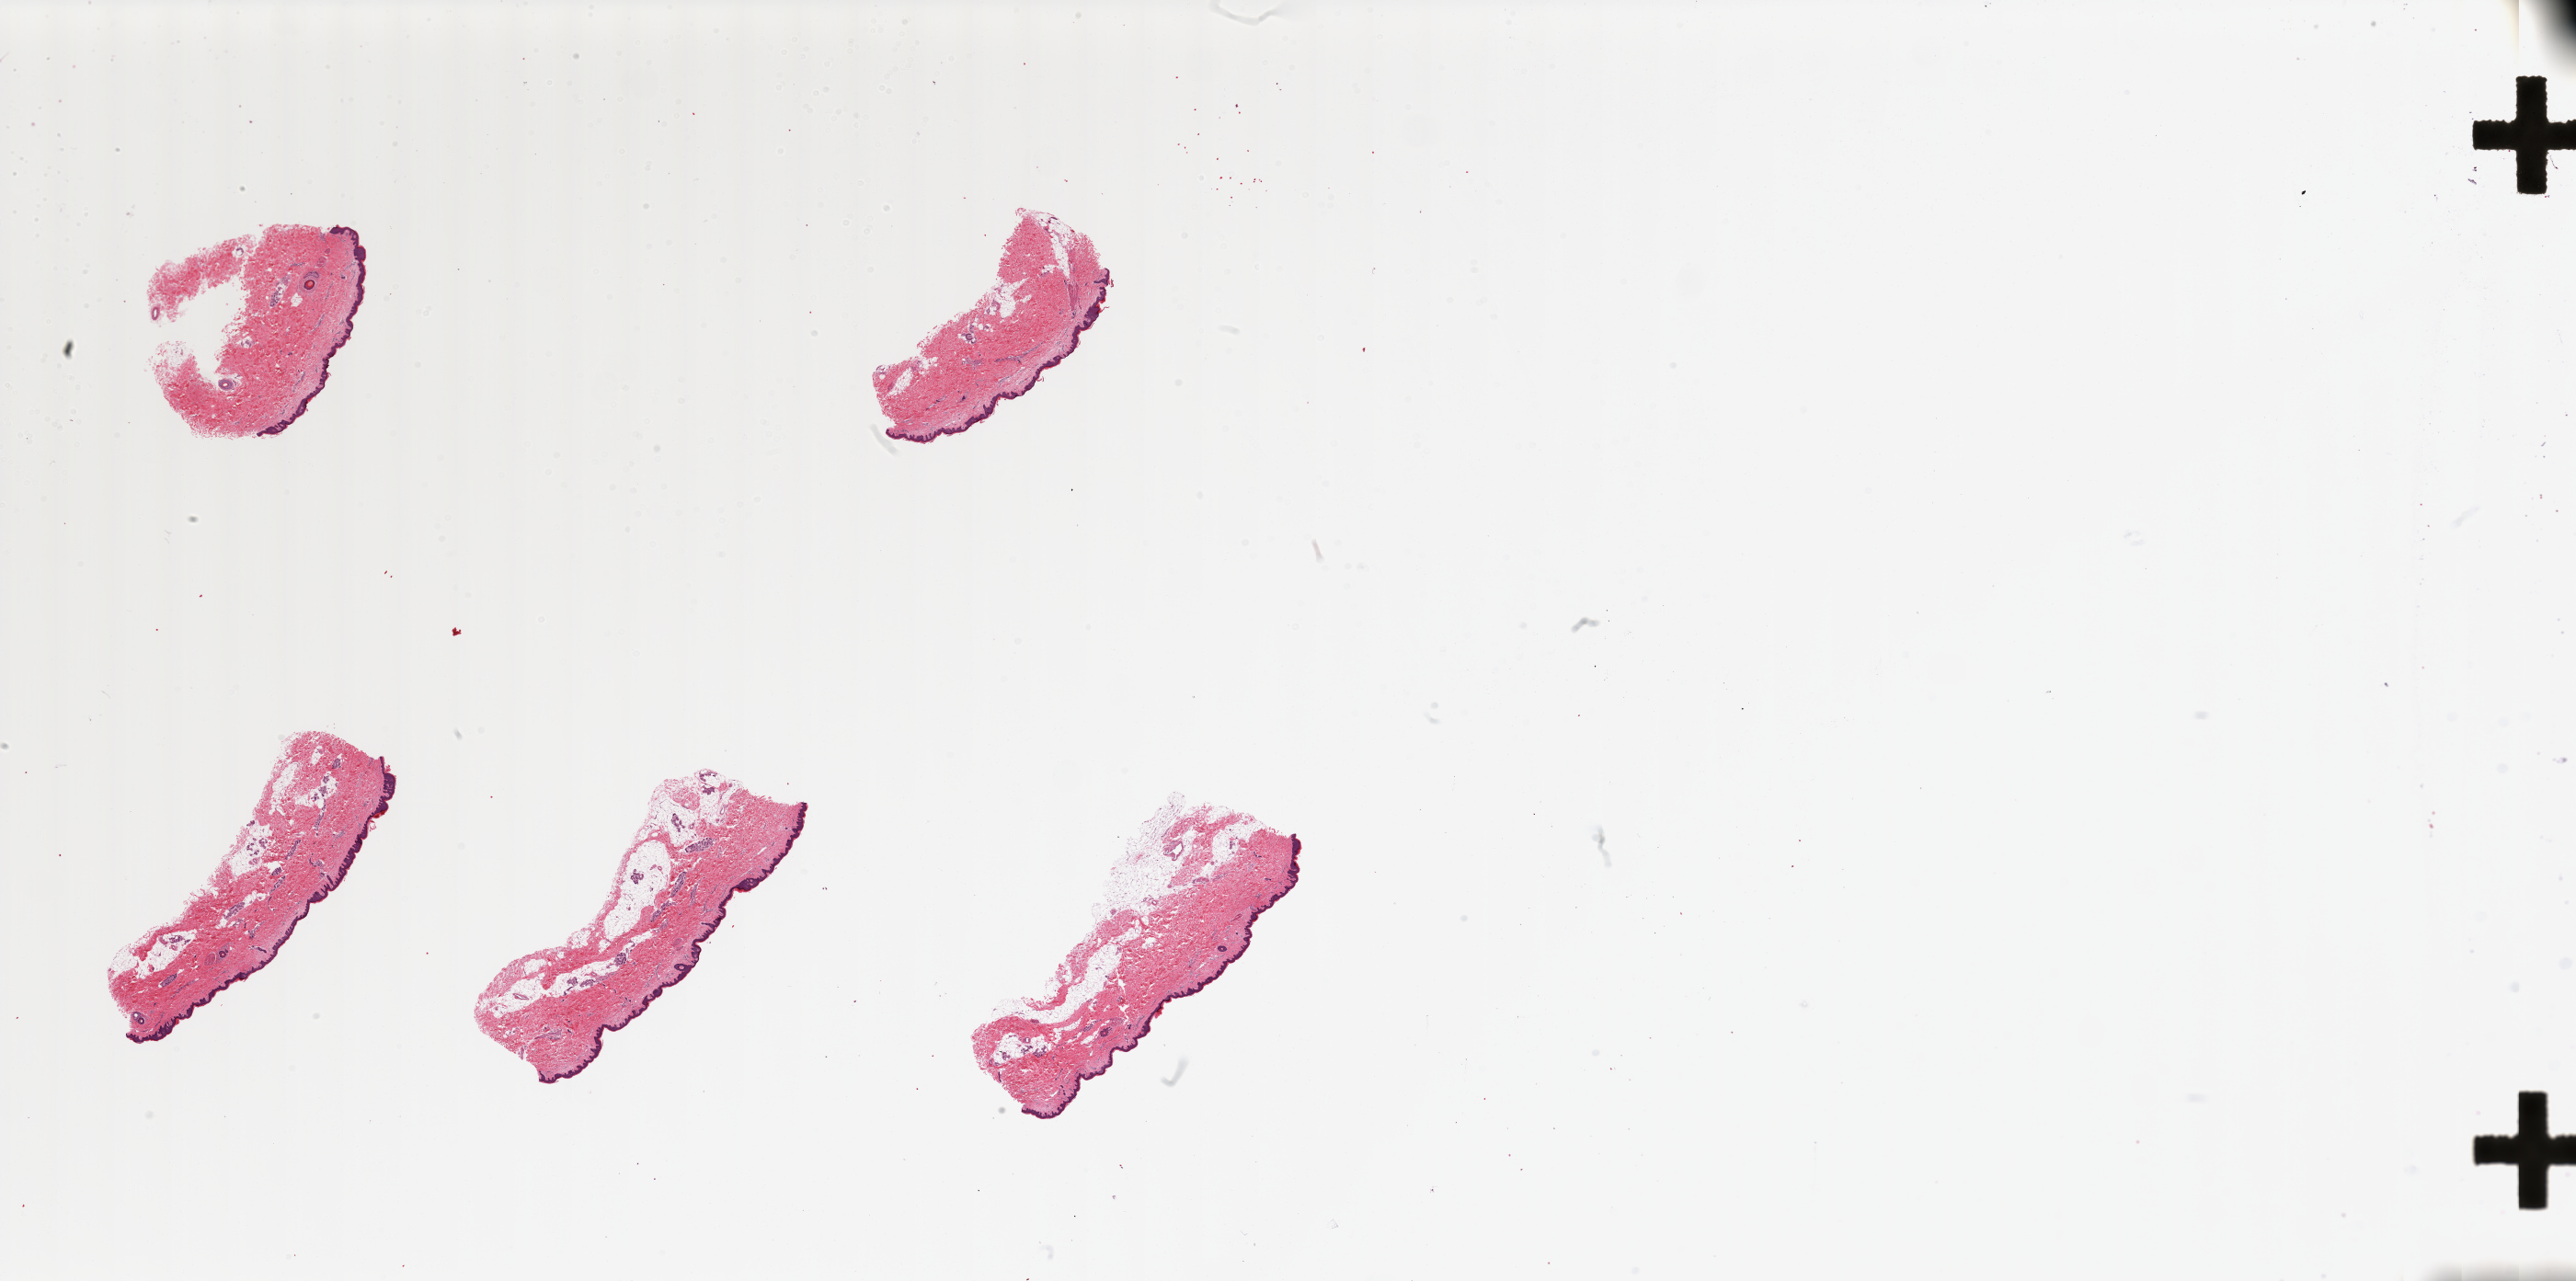
Whole-slide image, hematoxylin and eosin (H&E) stain — whole scanned area (about 44.3 x 22.0 mm, from a 20x scan) shown as a low-resolution overview, PAXgene-fixed paraffin-embedded (PFPE) section, section of skin of lower leg (target tissue), tissue donor sample. Donor sex: female.
Reviewer comment on this tissue sample: 5 pieces, include up to 30% attached and internal fat, squamous epithelium is 30-45 microns thick.